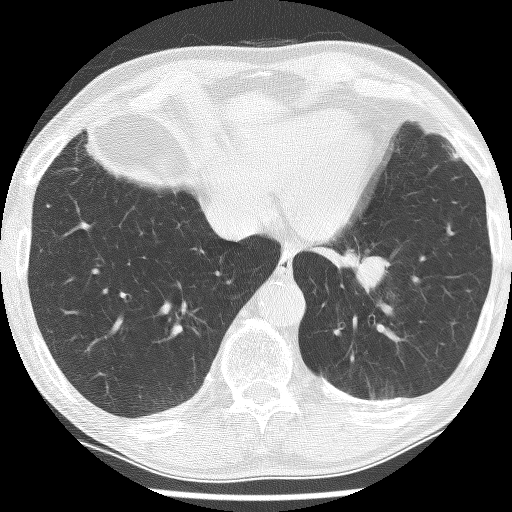
Low-dose screening chest CT, one axial slice. Lung window (W 1500 / L -600 HU). 2.5 mm slice thickness. 512 × 512 image matrix, field of view 320 × 320 mm.
Structures marked on this image (manually delineated by an expert):
- lesion 1 (tumor, lower lobe of left lung): box from (x=343, y=249) to (x=390, y=293) px